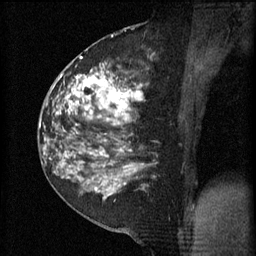
Breast MRI (dynamic contrast-enhanced), one sagittal slice; slice 25 of 60 in the series (ordered by position); 3 images stored at this slice position (order not interpretable as contrast timing); 1.5 T; TE 4.2 ms, TR 11 ms; 2 mm slice thickness; 256 × 256 image matrix. Female patient, age 52 years.
Structures marked on this image (semi-automatic segmentation, software-assisted and operator-edited):
- analysis volume of interest (the breast-tissue region the enhancement analysis was run in; not a lesion): bounding box <81,54,145,157> (left, top, right, bottom; pixels)
- tumour enhancement mask (voxels above the 70 % enhancement threshold inside the analysis volume of interest): <81,58,144,157>